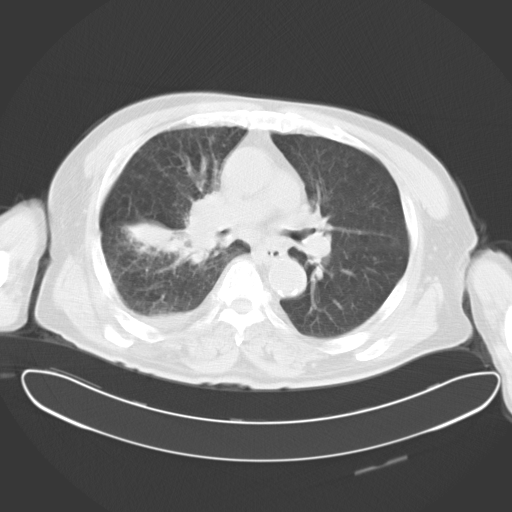
Chest CT, one axial slice. Position 17 of 30 along the scan axis. Reconstruction kernel B40f. Lung window (W 1500 / L -600 HU). 10 mm slice thickness. 512 × 512 image matrix, field of view 427 × 427 mm. Patient: male, 78 years. Case-level facts recorded for this patient, not image findings: clinical TNM (as recorded): T2 N1 M1.
Outlined on this slice (rectangle marked by the reading radiologist):
- lung tumour (recorded histology: adenocarcinoma): box from (x=115, y=186) to (x=234, y=270) px